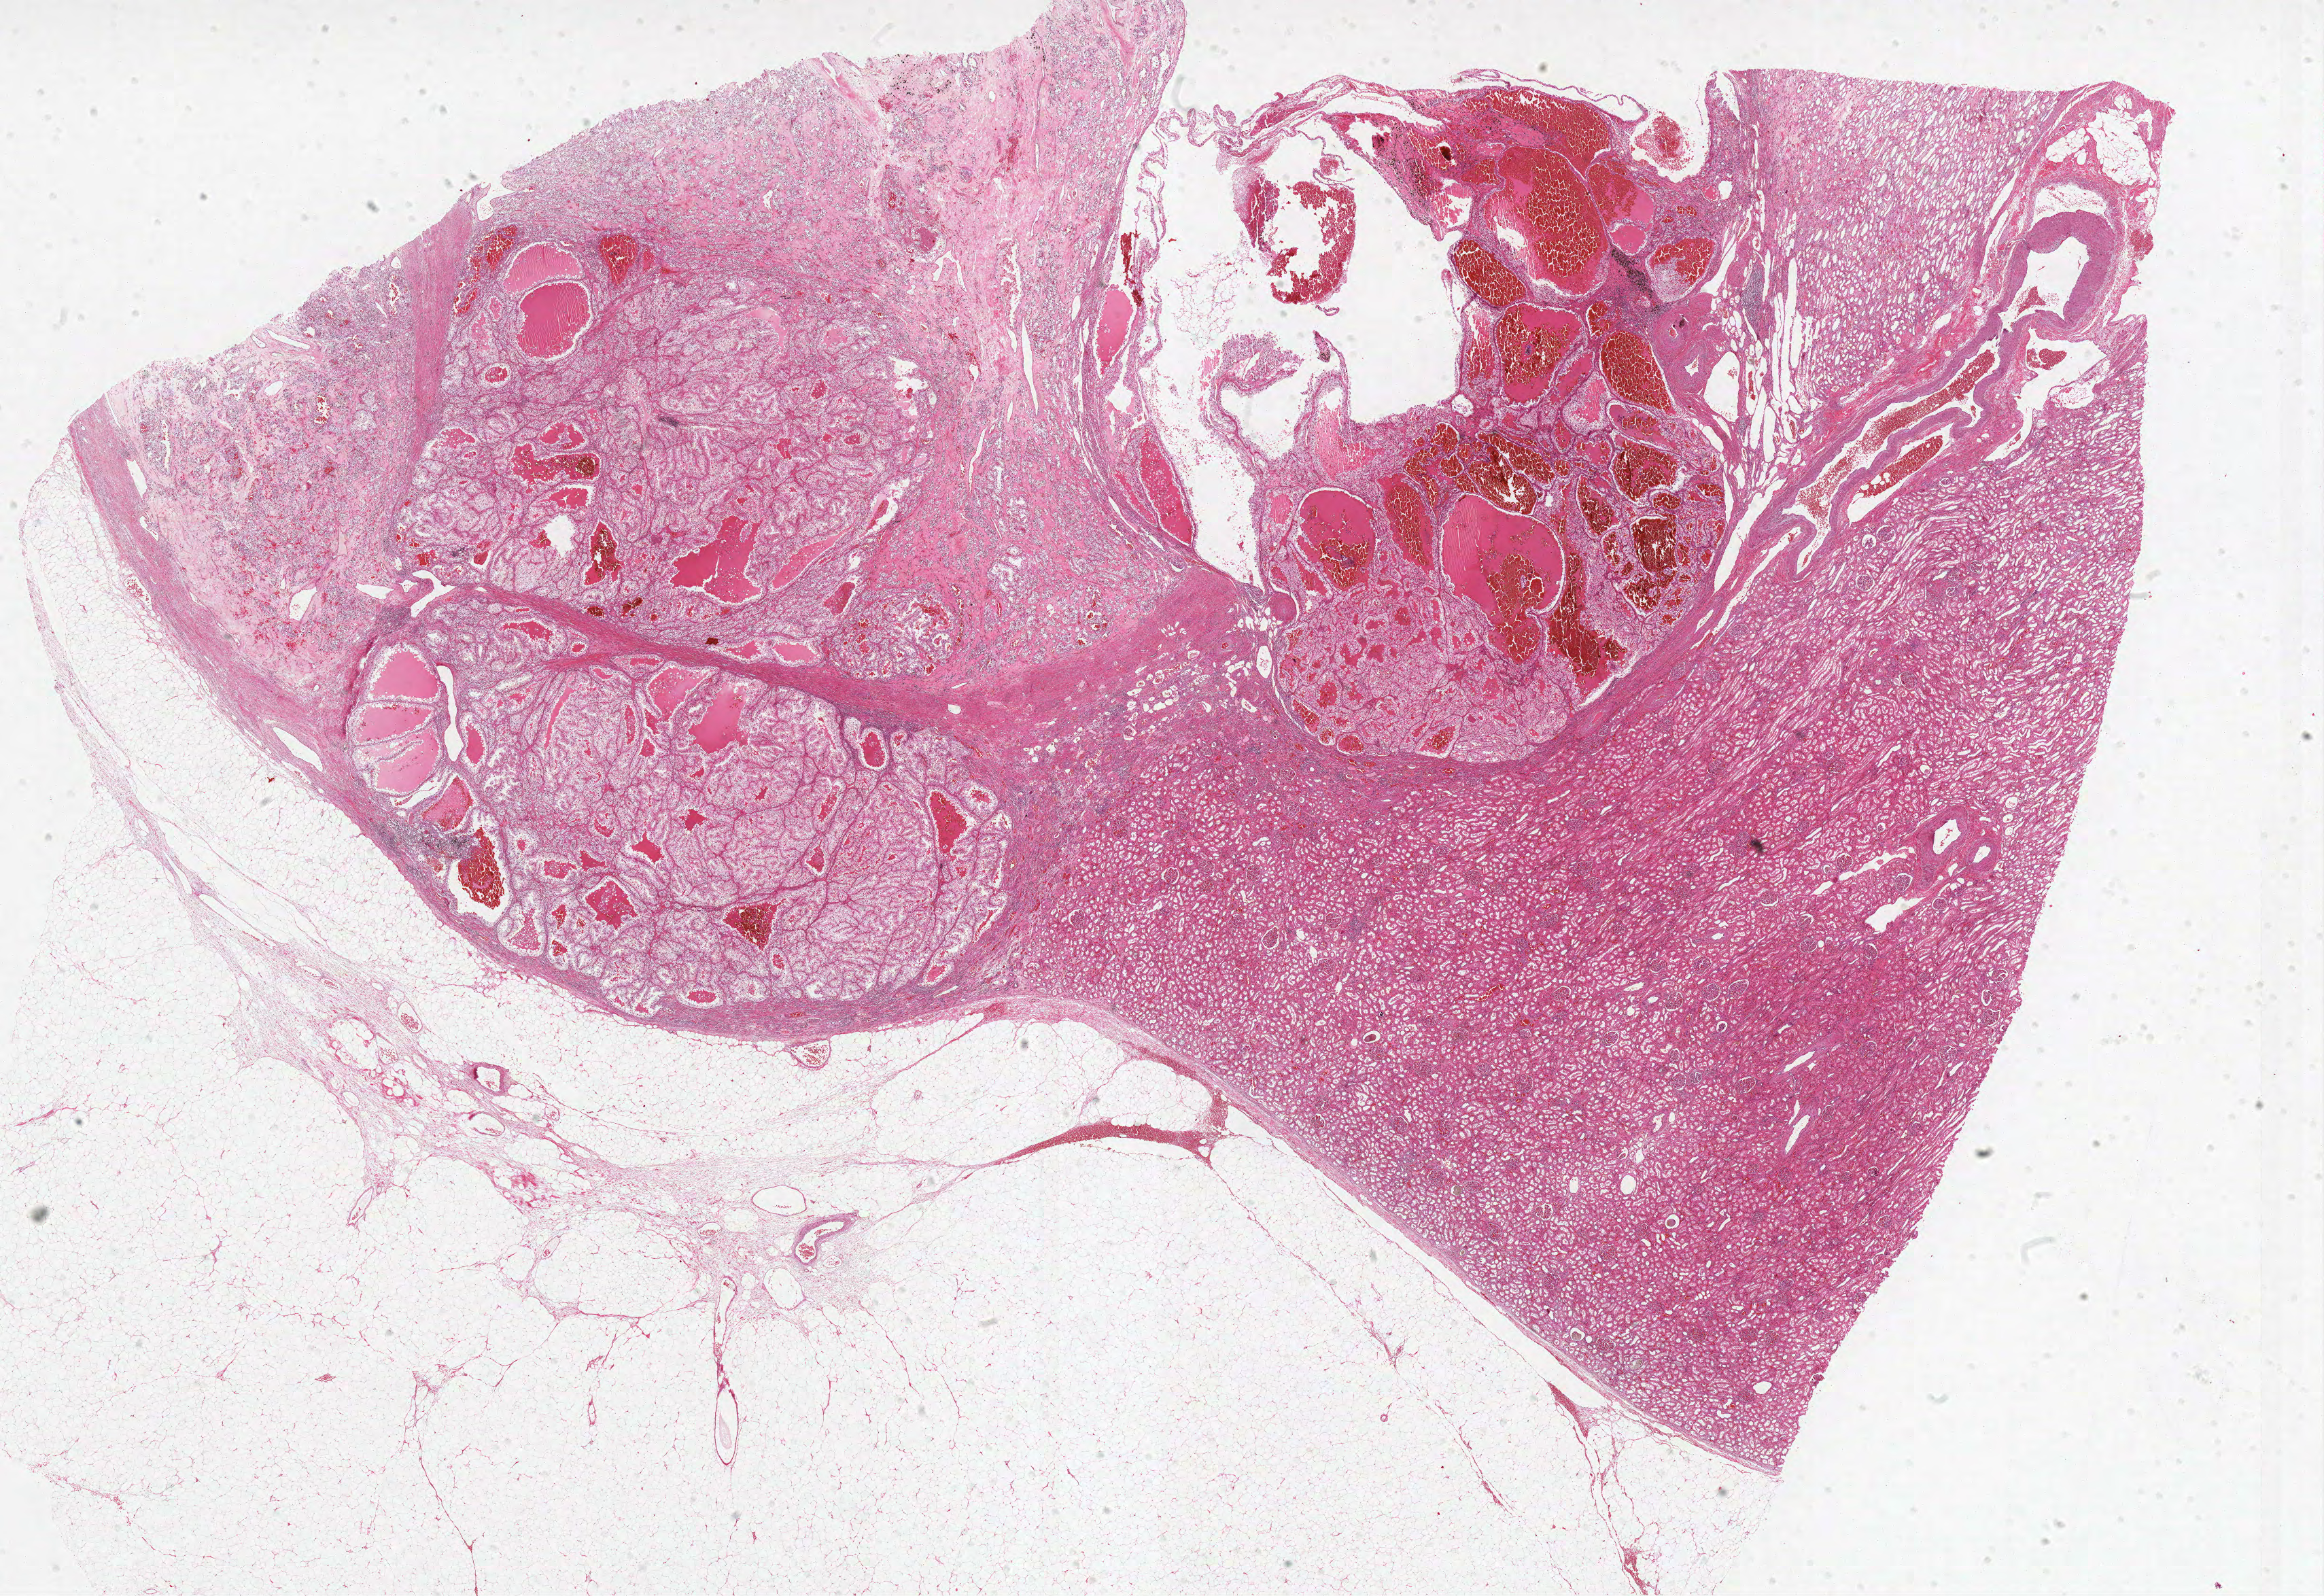
Hematoxylin and eosin (H&E) stained whole-slide image — a low-resolution overview of the entire scanned area, about 27.3 x 18.8 mm; formalin-fixed paraffin-embedded (FFPE) diagnostic section; sample: primary tumour, kidney. Patient: male, age at initial diagnosis 69 years. Histologic grade: G3 (poorly differentiated).
- laterality: left
- AJCC pathologic stage: III
- pathologic diagnosis: Clear cell adenocarcinoma, NOS